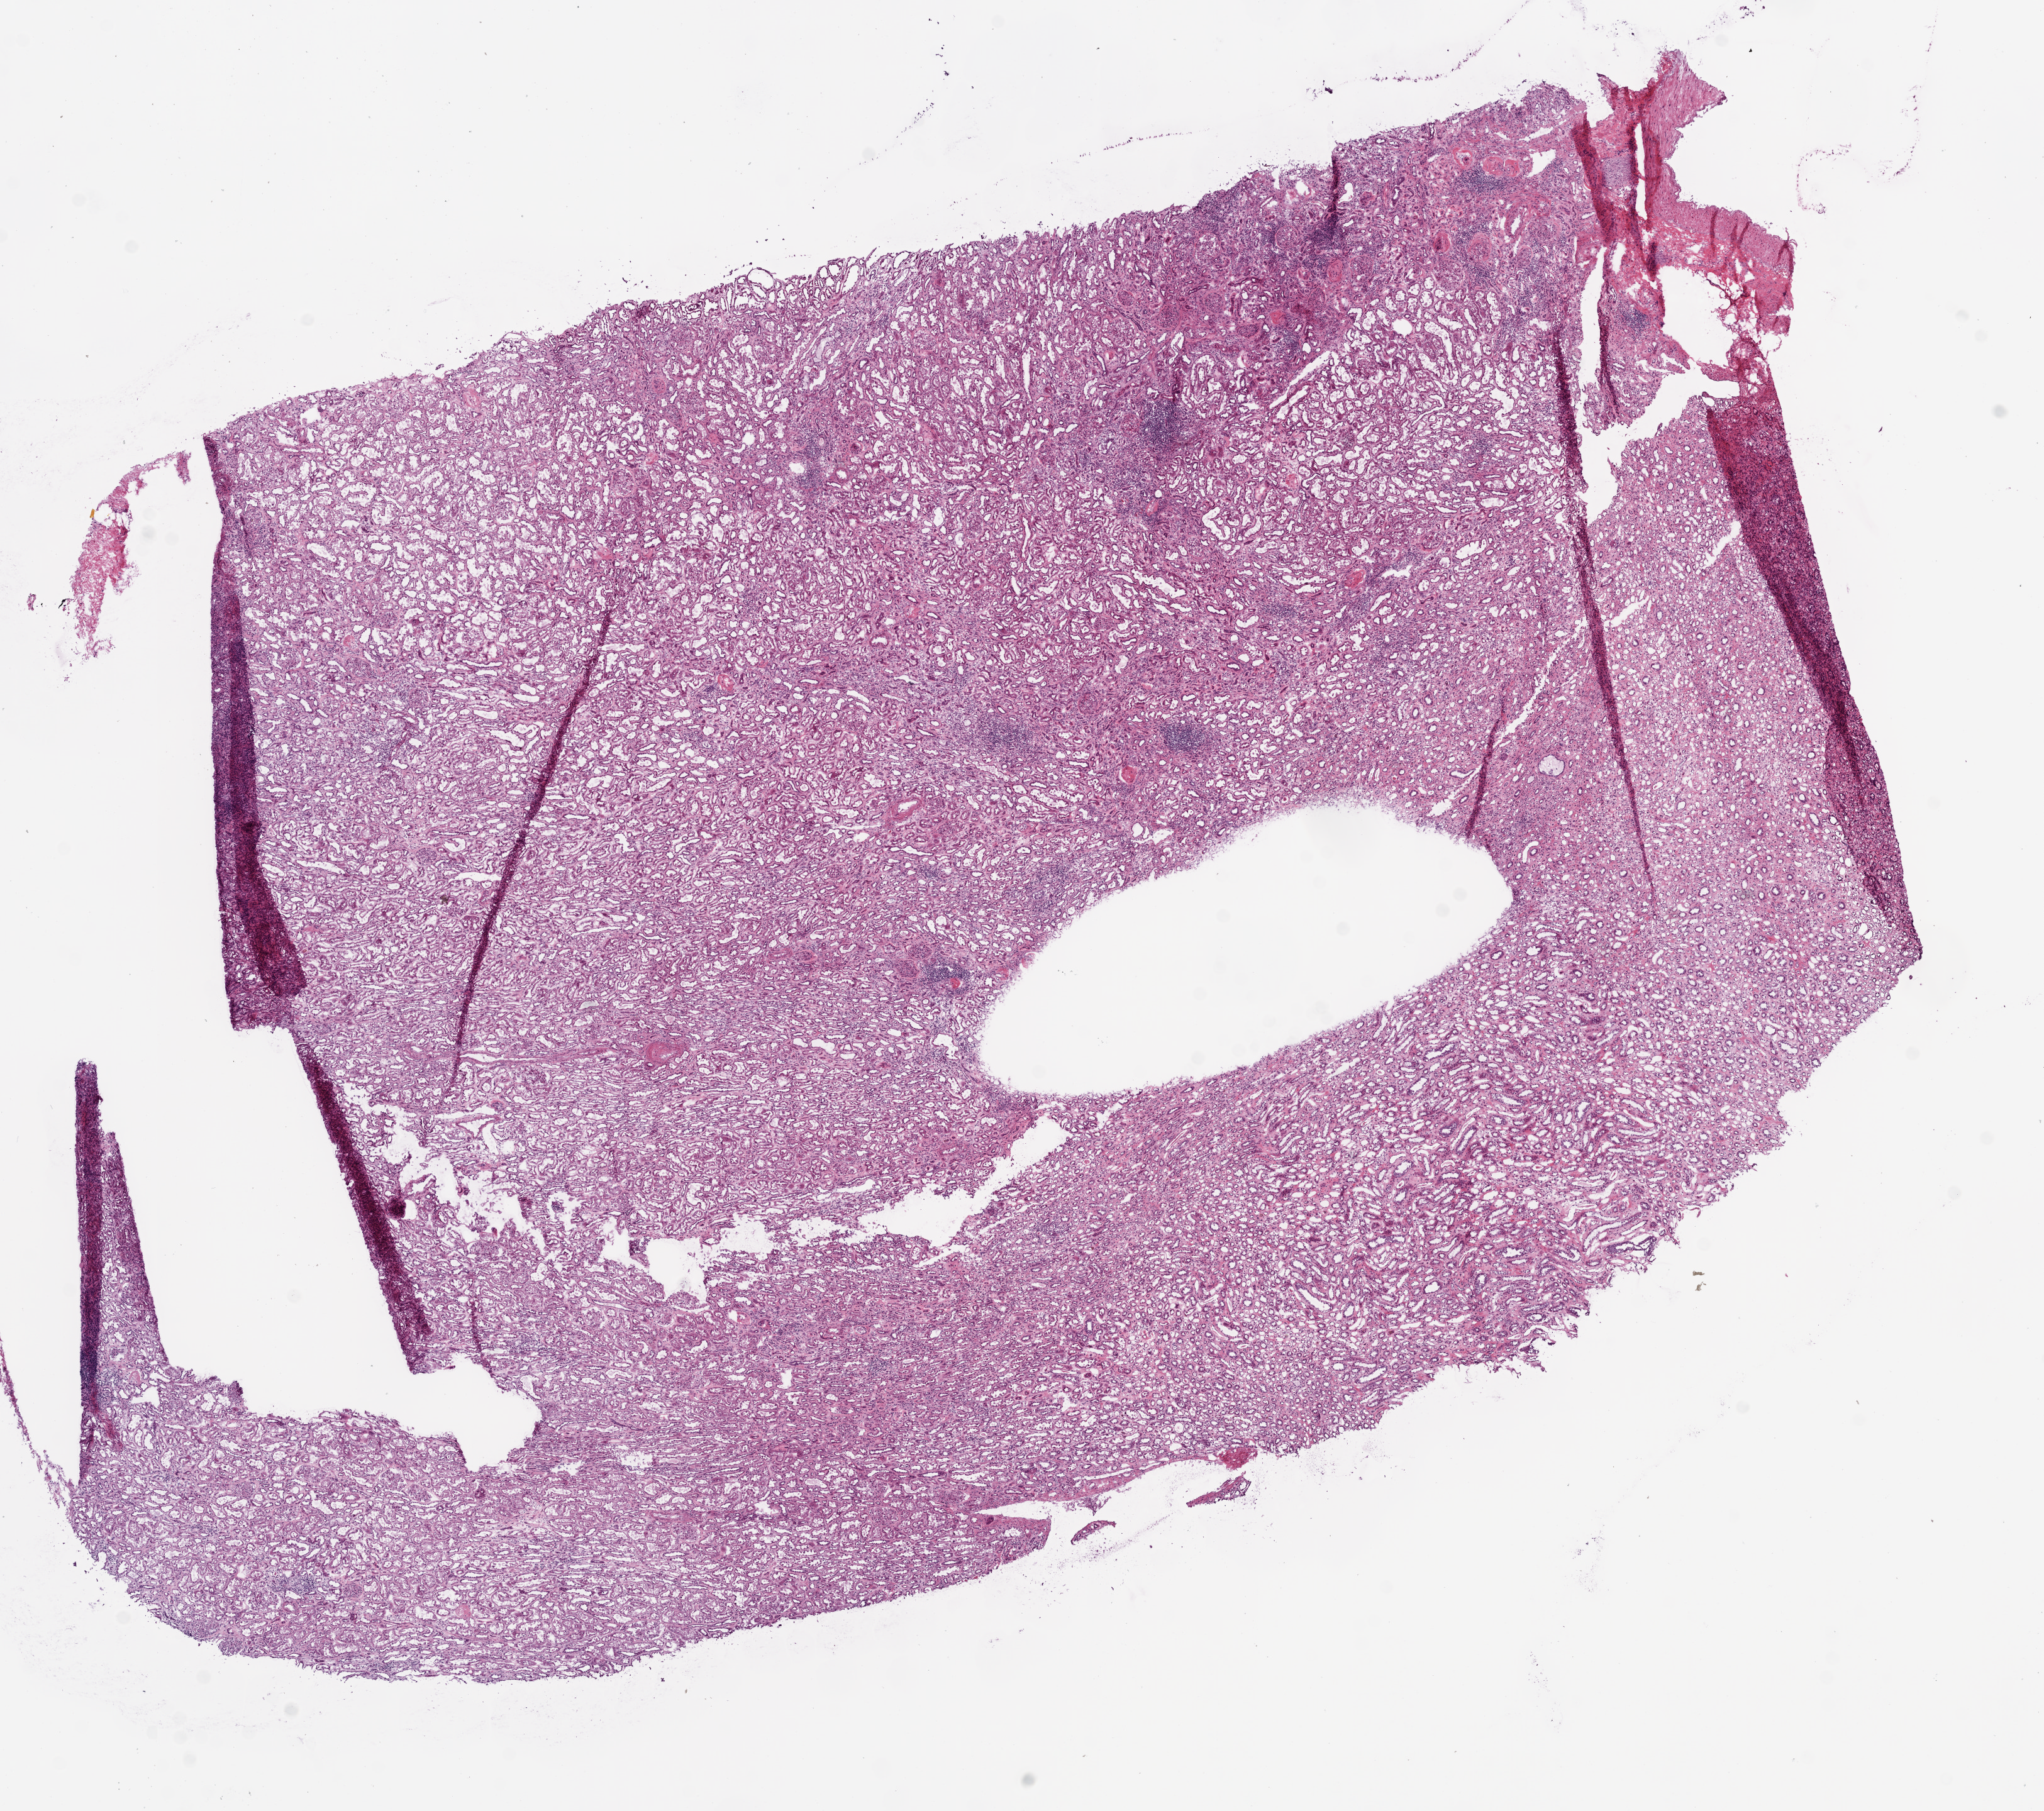
Whole-slide histology image, H&E — low-resolution overview of the scanned area, about 13.0 x 11.6 mm (slide scanned at 20x), frozen section from the bottom of the tissue portion, solid tissue normal (non-tumour tissue) sample from the kidney. Patient: male, age at initial diagnosis 52 years.
This section: solid tissue normal (non-tumour) sample from the same patient. Patient diagnosis: Clear cell adenocarcinoma, NOS.